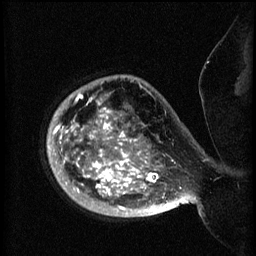
Breast MRI (dynamic contrast-enhanced), one sagittal slice; position 54 of 60 along the scan axis; 3 images stored at this slice position (order not interpretable as contrast timing); 1.5 T; TE 4.2 ms, TR 8.2 ms; 256 × 256 image matrix. Female patient, age 50 years.
Outlined on this slice (semi-automatically segmented with operator editing):
- analysis volume of interest (the breast-tissue region the enhancement analysis was run in; not a lesion): bounding box [x1, y1, x2, y2] px = [48, 76, 173, 217]
- tumour enhancement mask (voxels above the 70 % enhancement threshold inside the analysis volume of interest): [48, 94, 173, 215]